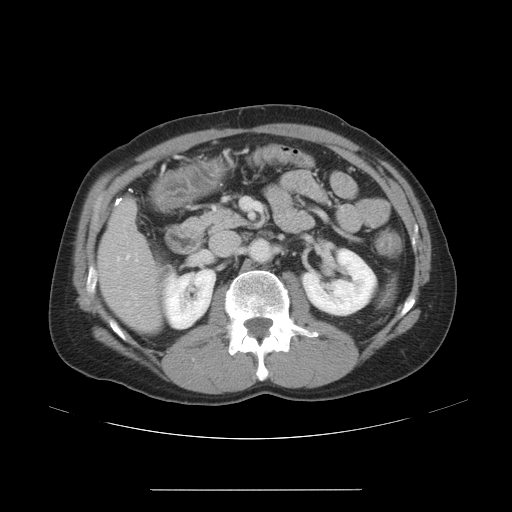
Contrast-enhanced abdominal CT, one axial slice; slice 21 of 48 in the series (ordered by position); 120 kVp; soft-tissue window (W 400 / L 40 HU); 5 mm slice thickness; 512 × 512 image matrix. Male patient, age 56 years. Case-level facts recorded for this patient, not image findings: diagnosis: colorectal cancer liver metastases, imaged before liver resection; multiple liver metastases: yes; largest metastasis: 1.8 cm; disease in both lobes: yes.
Outlined on this slice (manually delineated by an expert):
- hepatic veins: bounding box <125,253,131,305> (left, top, right, bottom; pixels)
- liver: <99,203,159,332>
- planned liver remnant (the part of the liver to remain after resection): <101,268,159,331>